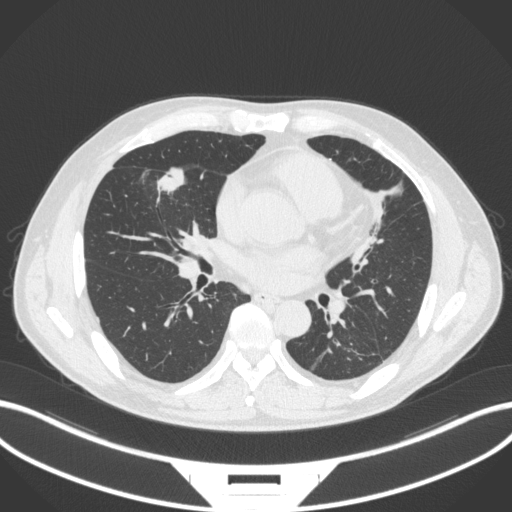
Chest CT, one axial slice; position 148 of 399 along the scan axis; reconstruction kernel B31f; 120 kVp; lung window (W 1500 / L -600 HU); 1 mm slice thickness; 512 × 512 image matrix. Male patient, age 59 years. Case-level facts recorded for this patient, not image findings: clinical TNM (as recorded): T2a N1 M0.
Annotated regions visible in this slice (rectangle marked by the reading radiologist):
- lung tumour (recorded histology: adenocarcinoma): bounding box [x1, y1, x2, y2] px = [151, 163, 190, 195]